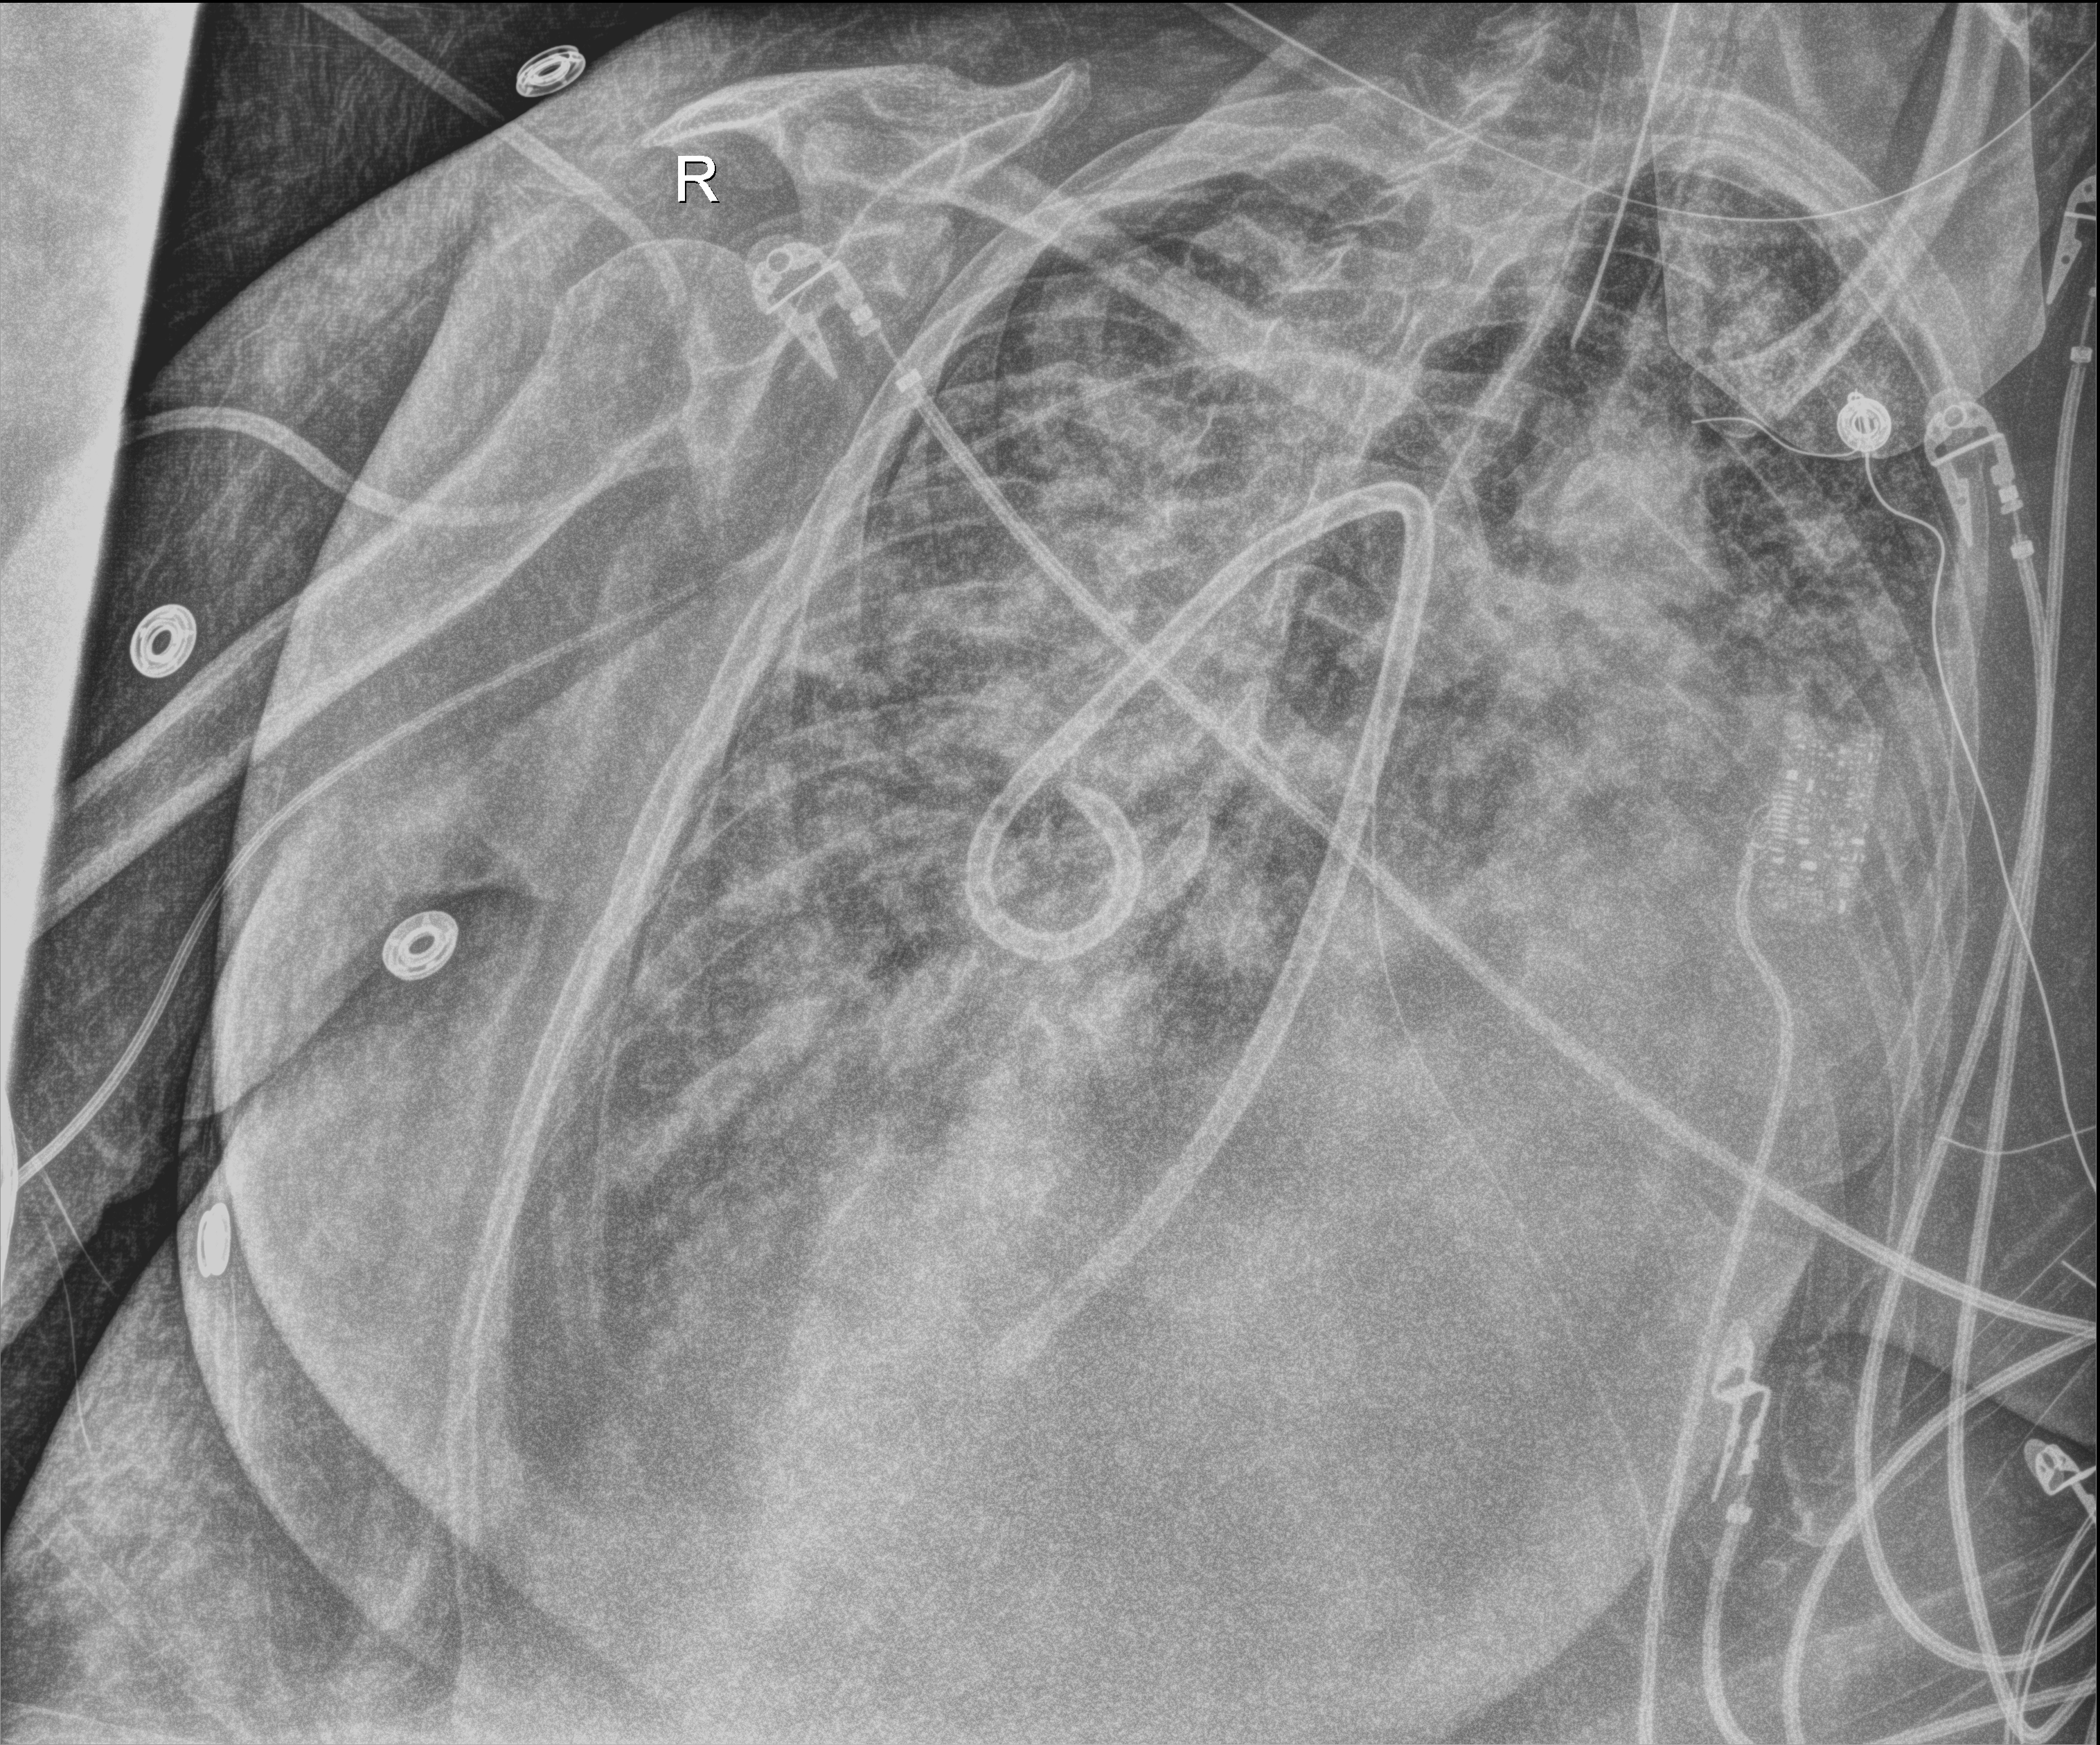
Portable chest radiograph. Adult patient hospitalised with COVID-19, age 18–59 years.
Admission-level facts for this patient (not findings on this image; timing relative to this image not recorded):
- mechanically ventilated during this hospital stay: yes
- admitted to intensive care during this hospital stay: yes